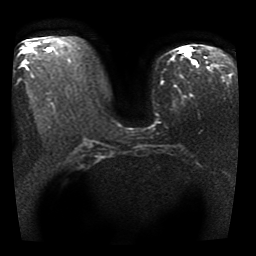
Breast MRI, one axial slice. Position 17 of 41 along the scan axis. Diffusion-weighted series; image 2 of 4 stored at this slice position (different b-values; order by instance number). 1.5 T. 5 mm slice thickness. 256 × 256 image matrix, field of view 330 × 330 mm. Female patient.
Annotated regions visible in this slice (manually delineated by an expert):
- tumour on diffusion-weighted imaging: bounding box <185,52,196,65> (left, top, right, bottom; pixels)